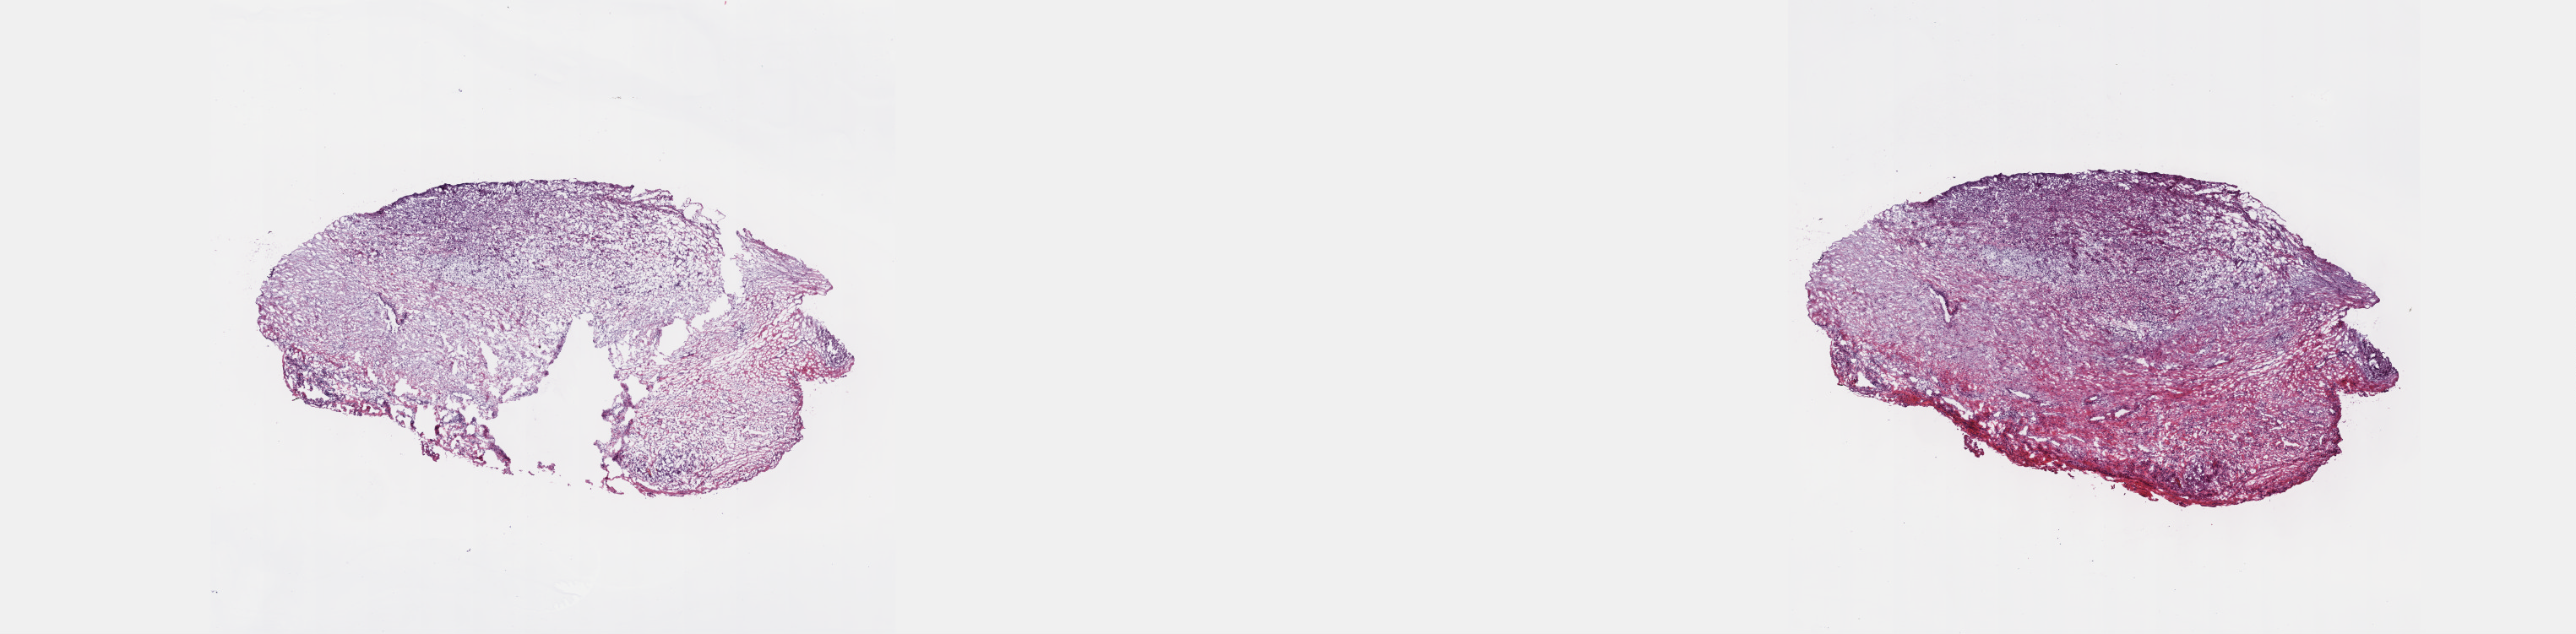
Whole-slide histology image, H&E-stained, shown as a low-resolution overview of the whole scanned area (about 24.6 x 6.1 mm). Frozen section from the top of the tissue portion. Primary tumour sample from the connective, subcutaneous and other soft tissues. Male patient; age at initial diagnosis 52 years. Composition of this section per pathologist review: tumour cells 60%, tumour nuclei 60%, normal cells 0%, stromal cells 40%, necrosis 0%. Inflammatory infiltration, as recorded: lymphocyte infiltration 0%, monocyte infiltration 0%, neutrophil infiltration 0%.
Diagnosis: Malignant peripheral nerve sheath tumor (connective, subcutaneous and other soft tissues of trunk, NOS).